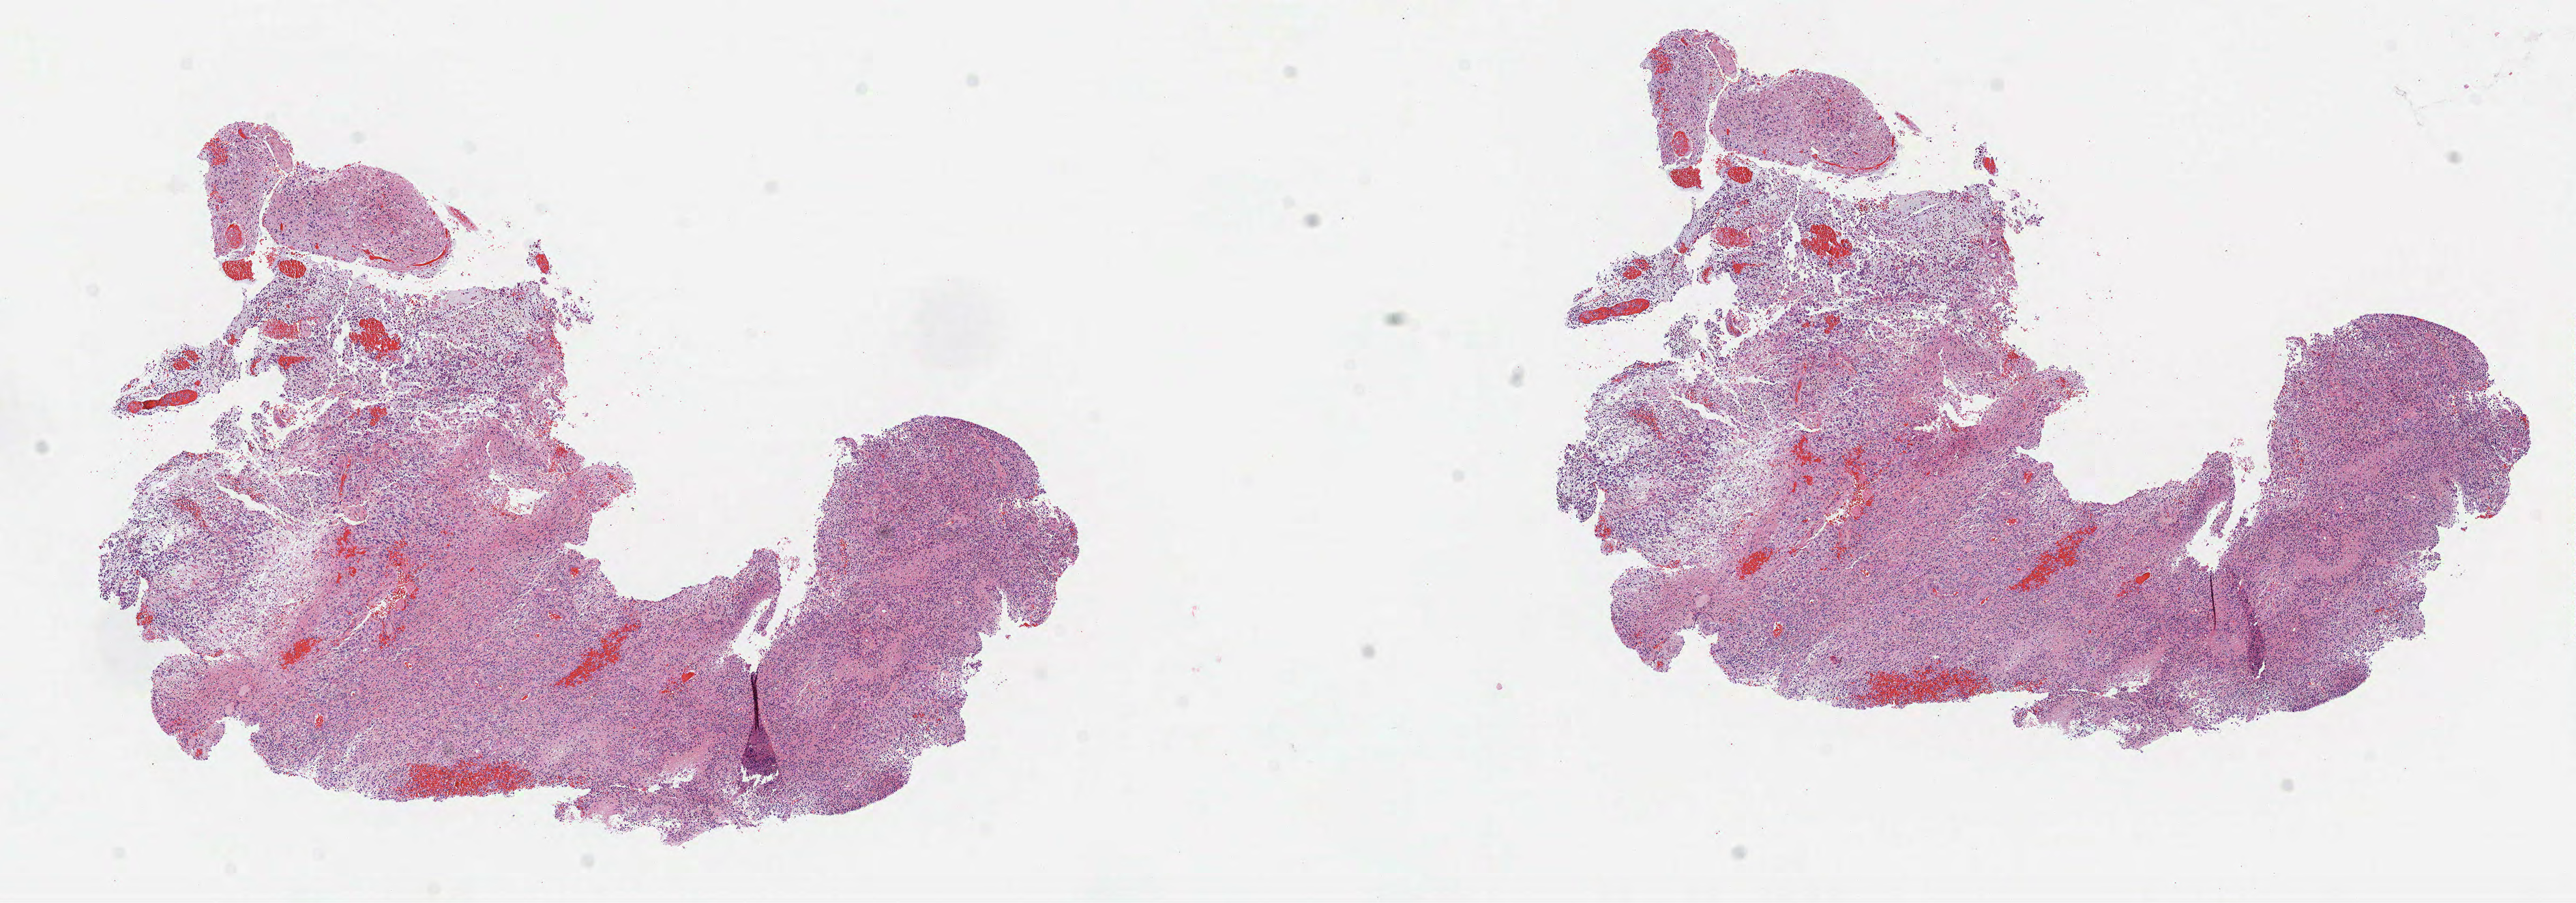
Whole-slide histology image, H&E — low-resolution overview of the scanned area, about 15.2 x 5.3 mm, FFPE section, primary tumour sample from the brain. Patient: male, age at initial diagnosis 58 years.
Diagnosis: Glioblastoma.